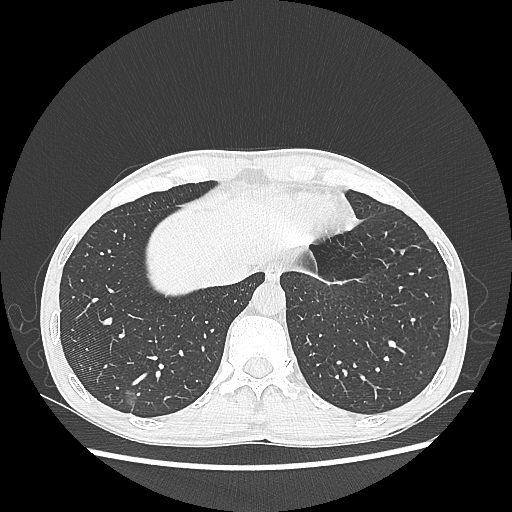
Chest CT, one axial slice; slice 62 of 270 in the series (ordered by position); 100 kVp; lung window (W 1500 / L -600 HU); 1.25 mm slice thickness; 512 × 512 image matrix. Patient: male, 60 years. From the clinical record (not read from this slice): clinical TNM (as recorded): T1c N0 M0.
Structures marked on this image (bounding box drawn by a radiologist):
- lung tumour (recorded histology: adenocarcinoma): box from (x=119, y=386) to (x=145, y=418) px